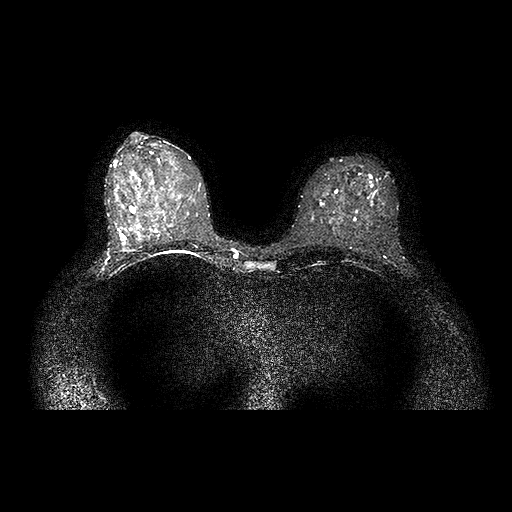
Breast MRI examination; 1 image, one mid-volume slice chosen by position.
Image 1: axial T2-weighted / STIR image, slice 45 of 88.
Pathology recorded for this patient (not read from these images): pathology diagnosis: benign fibrosis (left breast).